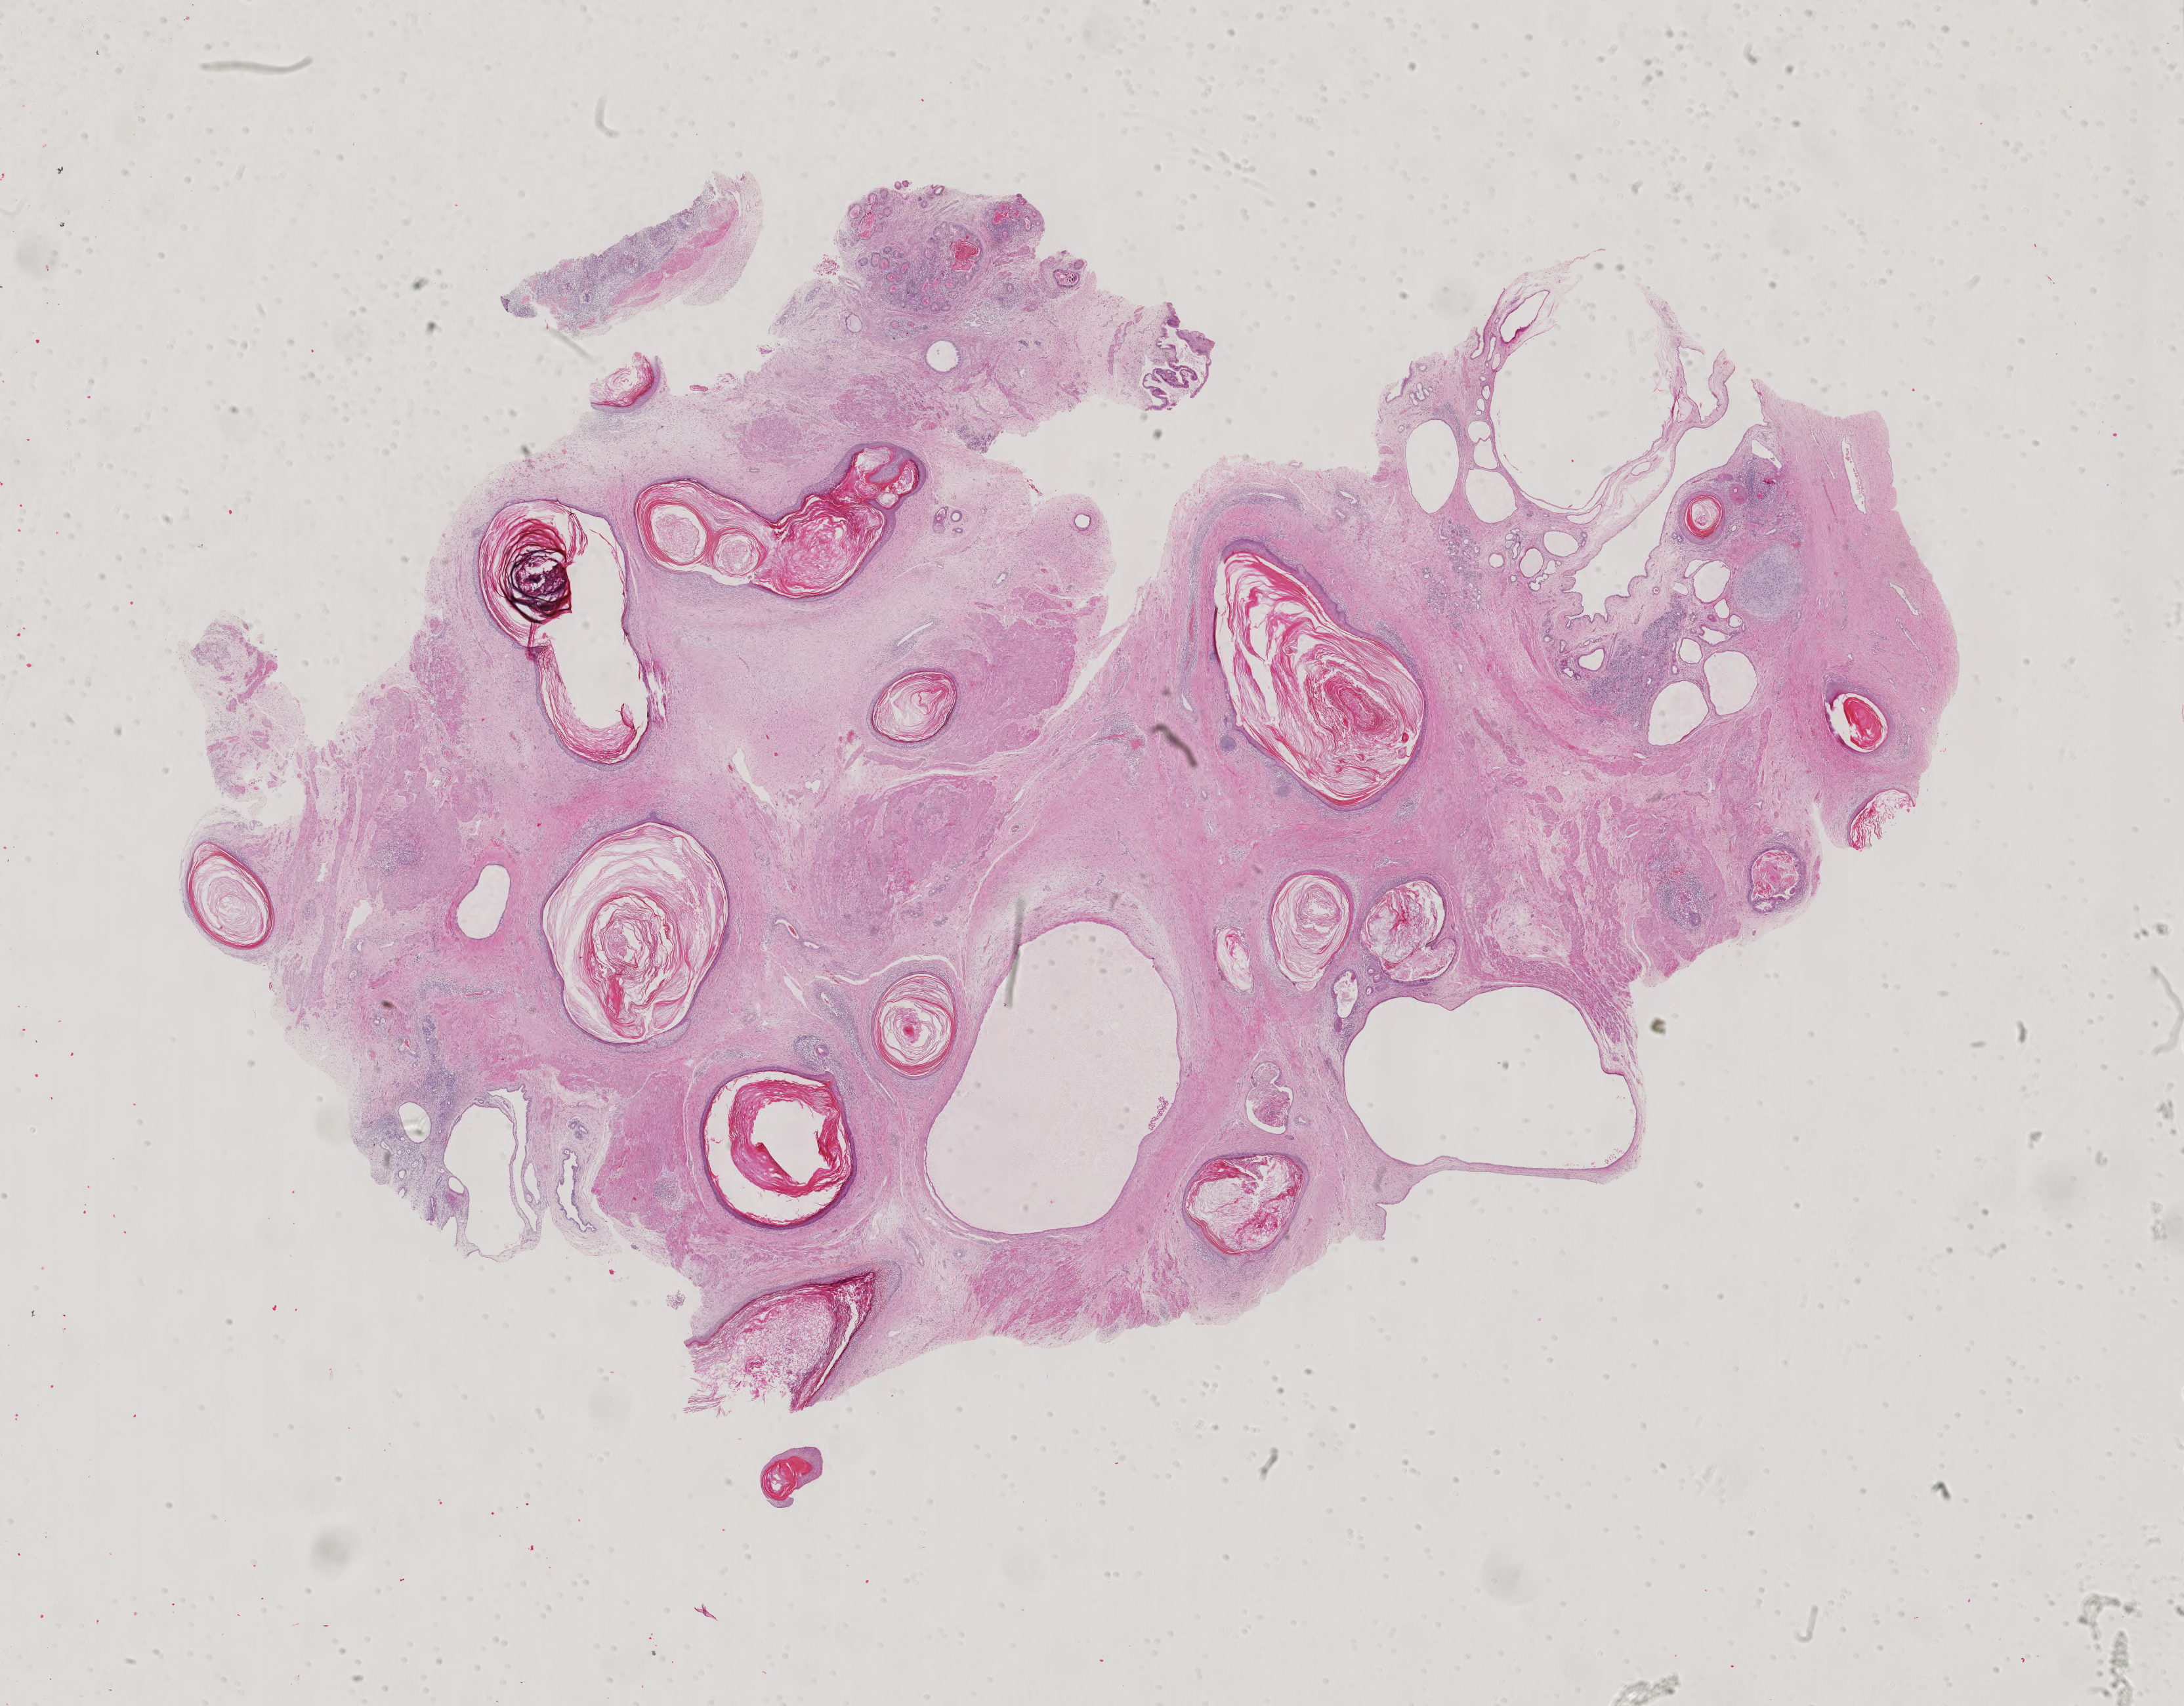
H&E whole-slide image, whole scanned area (about 24.2 x 18.9 mm) shown as a low-resolution overview; formalin-fixed paraffin-embedded (FFPE) diagnostic section; primary tumour sample from the testis. Male, age 24 years at initial diagnosis.
AJCC pathologic stage: IS (6th edition). Pathologic diagnosis: Teratoma, benign. Laterality: left.